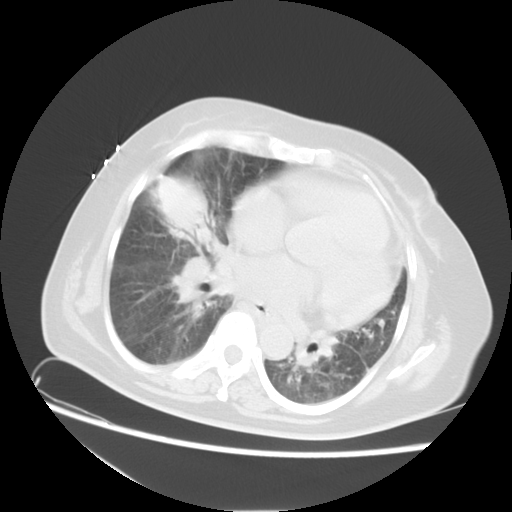
Chest CT, one axial slice; position 10 of 23 along the scan axis; lung window (W 1500 / L -600 HU); 512 × 512 image matrix, field of view 350 × 350 mm. Female patient, age 67 years. Case-level facts recorded for this patient, not image findings: clinical TNM (as recorded): T2a N3 M1a.
Outlined on this slice (rectangle marked by the reading radiologist):
- lung tumour (recorded histology: adenocarcinoma): bounding box <157,171,208,239> (left, top, right, bottom; pixels)